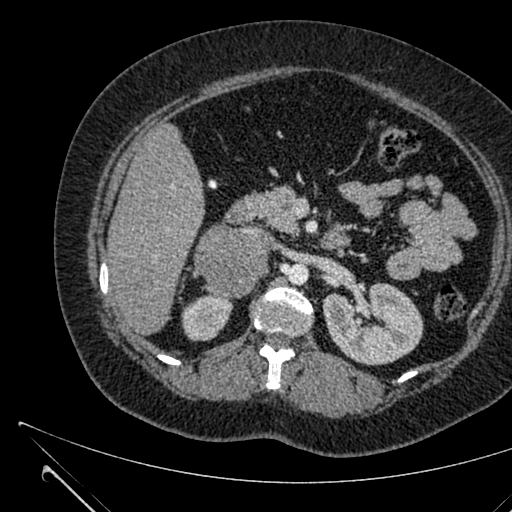
Contrast-enhanced abdominal CT, one axial slice. Position 376 of 731 along the scan axis. 120 kVp. Intravenous contrast given. Soft-tissue window (W 400 / L 40 HU). 1 mm slice thickness. 512 × 512 image matrix, field of view 376 × 376 mm. Female patient, age 36 years. Case-level facts recorded for this patient, not image findings: diagnosis: adrenocortical carcinoma; tumour side: right adrenal; tumour size at pathology: 10 cm.
Outlined on this slice (semi-automatically segmented with operator editing):
- mass: bounding box (x1, y1, x2, y2) in pixels: (193, 225, 268, 298)